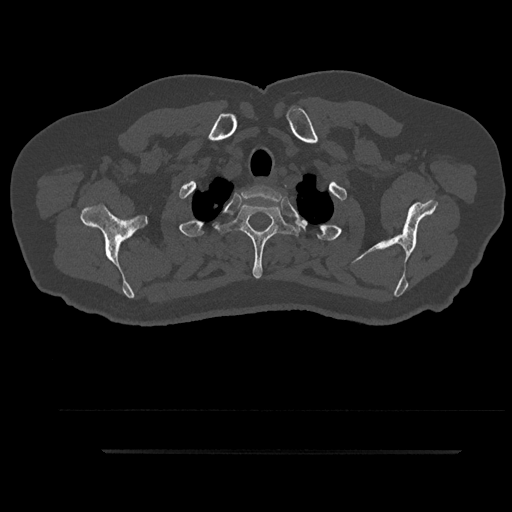
CT including the spine, one axial slice; slice 764 of 797 in the series (ordered by position); reconstruction kernel Br40s/3; bone window (W 1800 / L 400 HU); 512 × 512 image matrix, field of view 432 × 432 mm. Male patient, age 63 years. Case-level facts recorded for this patient, not image findings: primary cancer: renal.
Annotated regions visible in this slice (semi-automatically segmented with operator editing):
- T1 vertebra: bounding box [x1, y1, x2, y2] px = [238, 185, 283, 218]
- T2 vertebra: [216, 204, 303, 279]